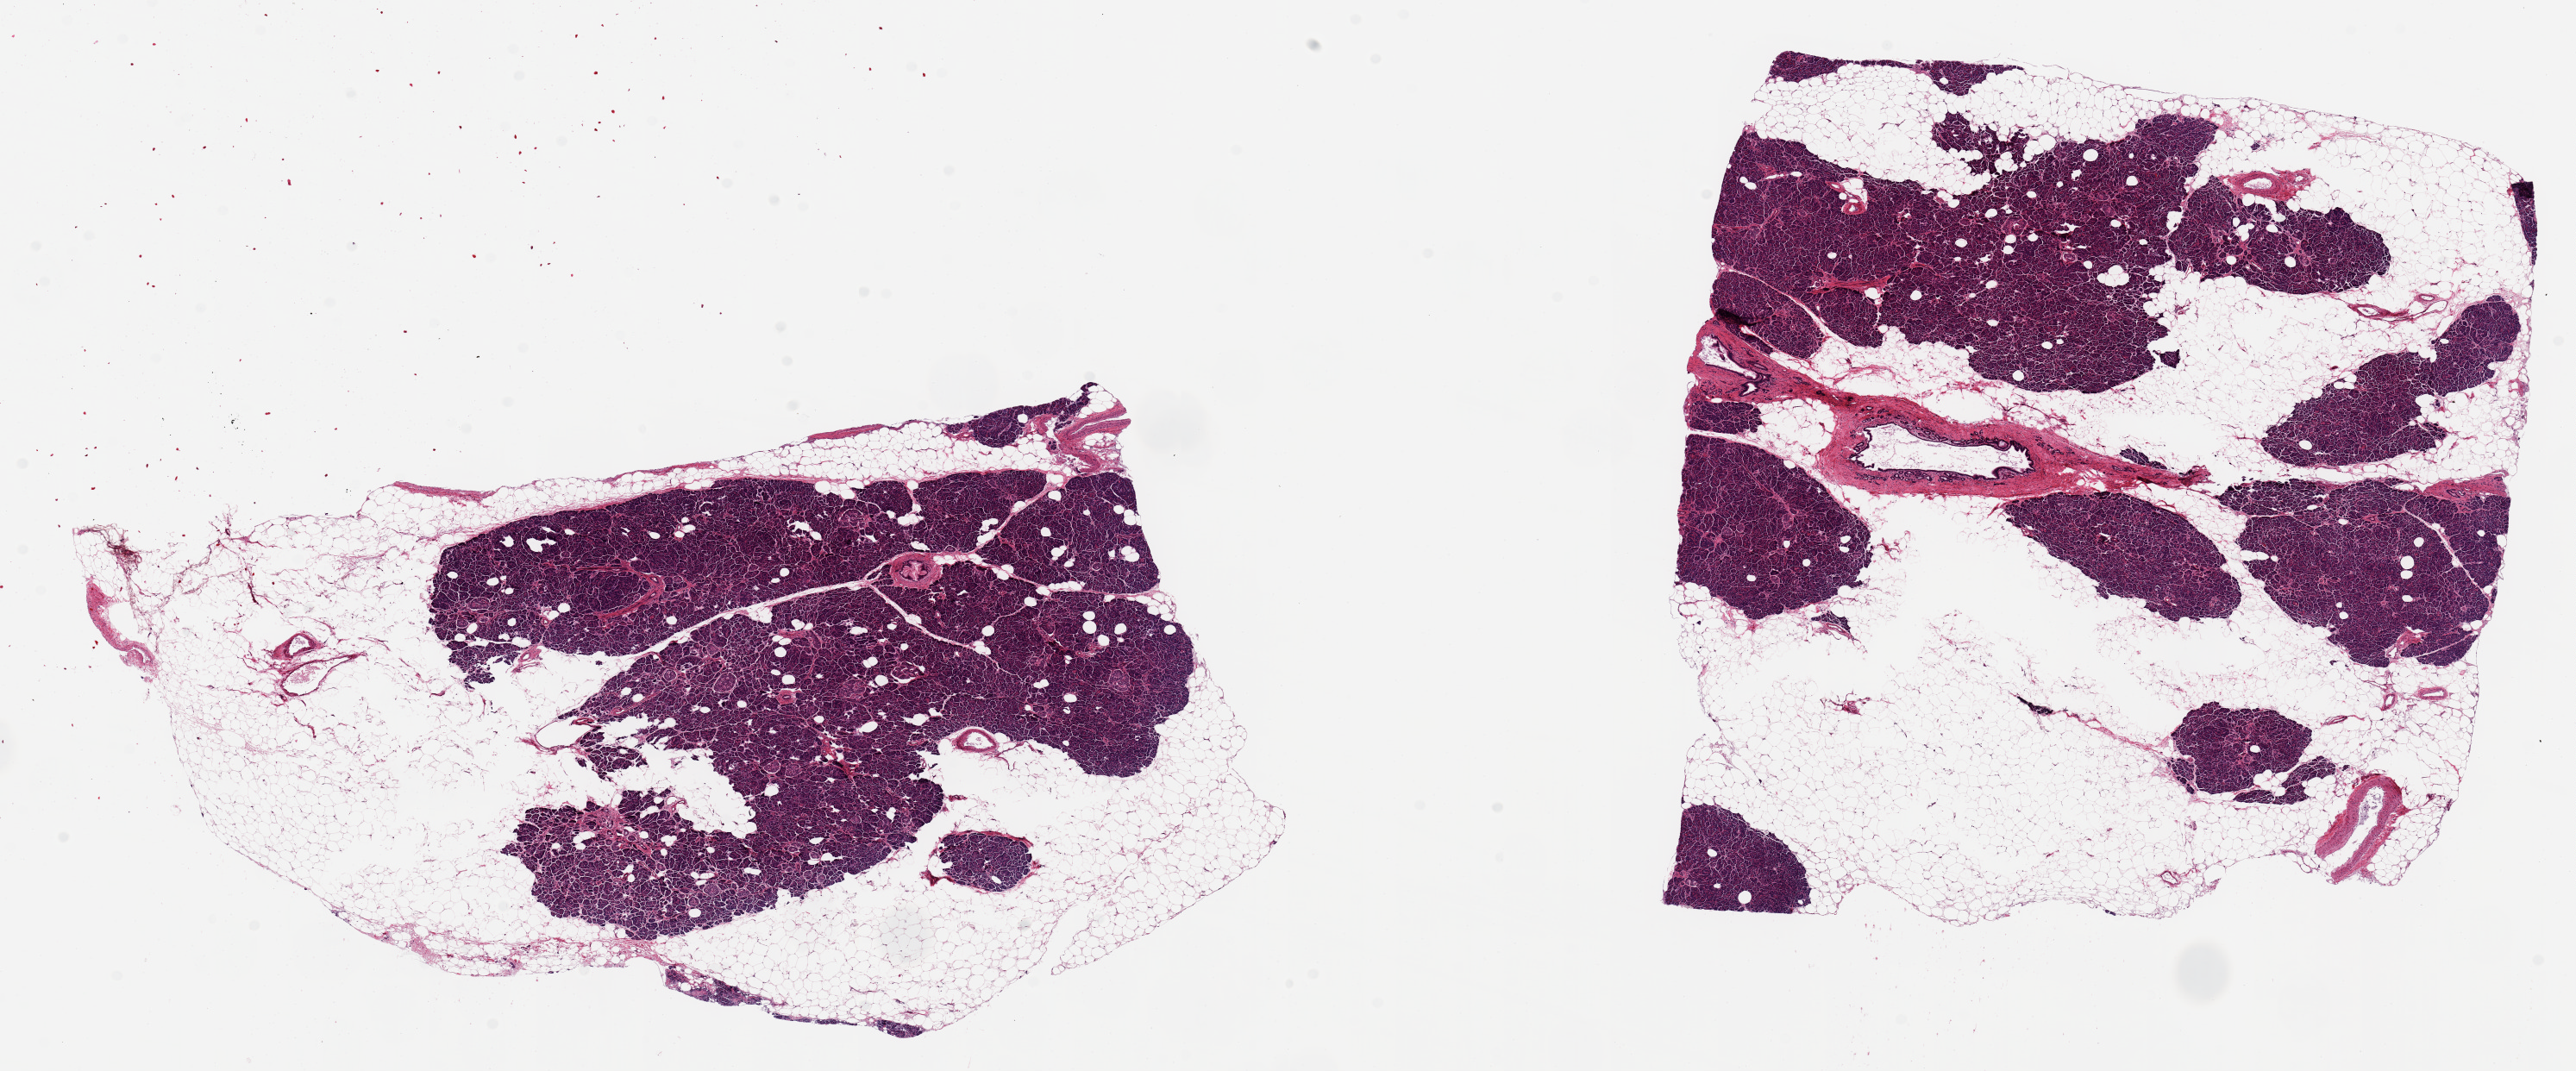
Digitized haematoxylin and eosin-stained section, brightfield, whole scanned area (about 23.6 x 9.8 mm, acquisition: 20x scan) shown as a low-resolution overview; PAXgene-fixed paraffin-embedded (PFPE) section; target tissue: pancreas; tissue donor sample. Male donor.
Reviewer comment on this tissue sample: 2 aliquots, ~9x6mm. Both with ~50% parenchyma, rest is intermingled/peripheral fat. Well preserved.